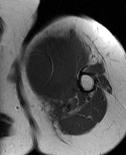
MRI of an extremity soft-tissue mass, one axial slice. Slice 55 of 86 in the series (ordered by position). MR volume resampled by the dataset authors to the PET/CT grid (not the native acquisition matrix). 3.27 mm slice thickness. 126 × 155 image matrix, field of view 123 × 151 mm. Female patient. Case-level facts recorded for this patient, not image findings: histological type: pleiomorphic leiomyosarcoma; grade: high; site of the primary tumour: left biceps.
Annotated regions visible in this slice (expert contour drawn on MRI and transferred to this co-registered scan by the dataset authors):
- gross tumour volume including surrounding oedema: bounding box [x1, y1, x2, y2] px = [24, 35, 83, 116]
- gross tumour volume (mass): [24, 35, 80, 100]